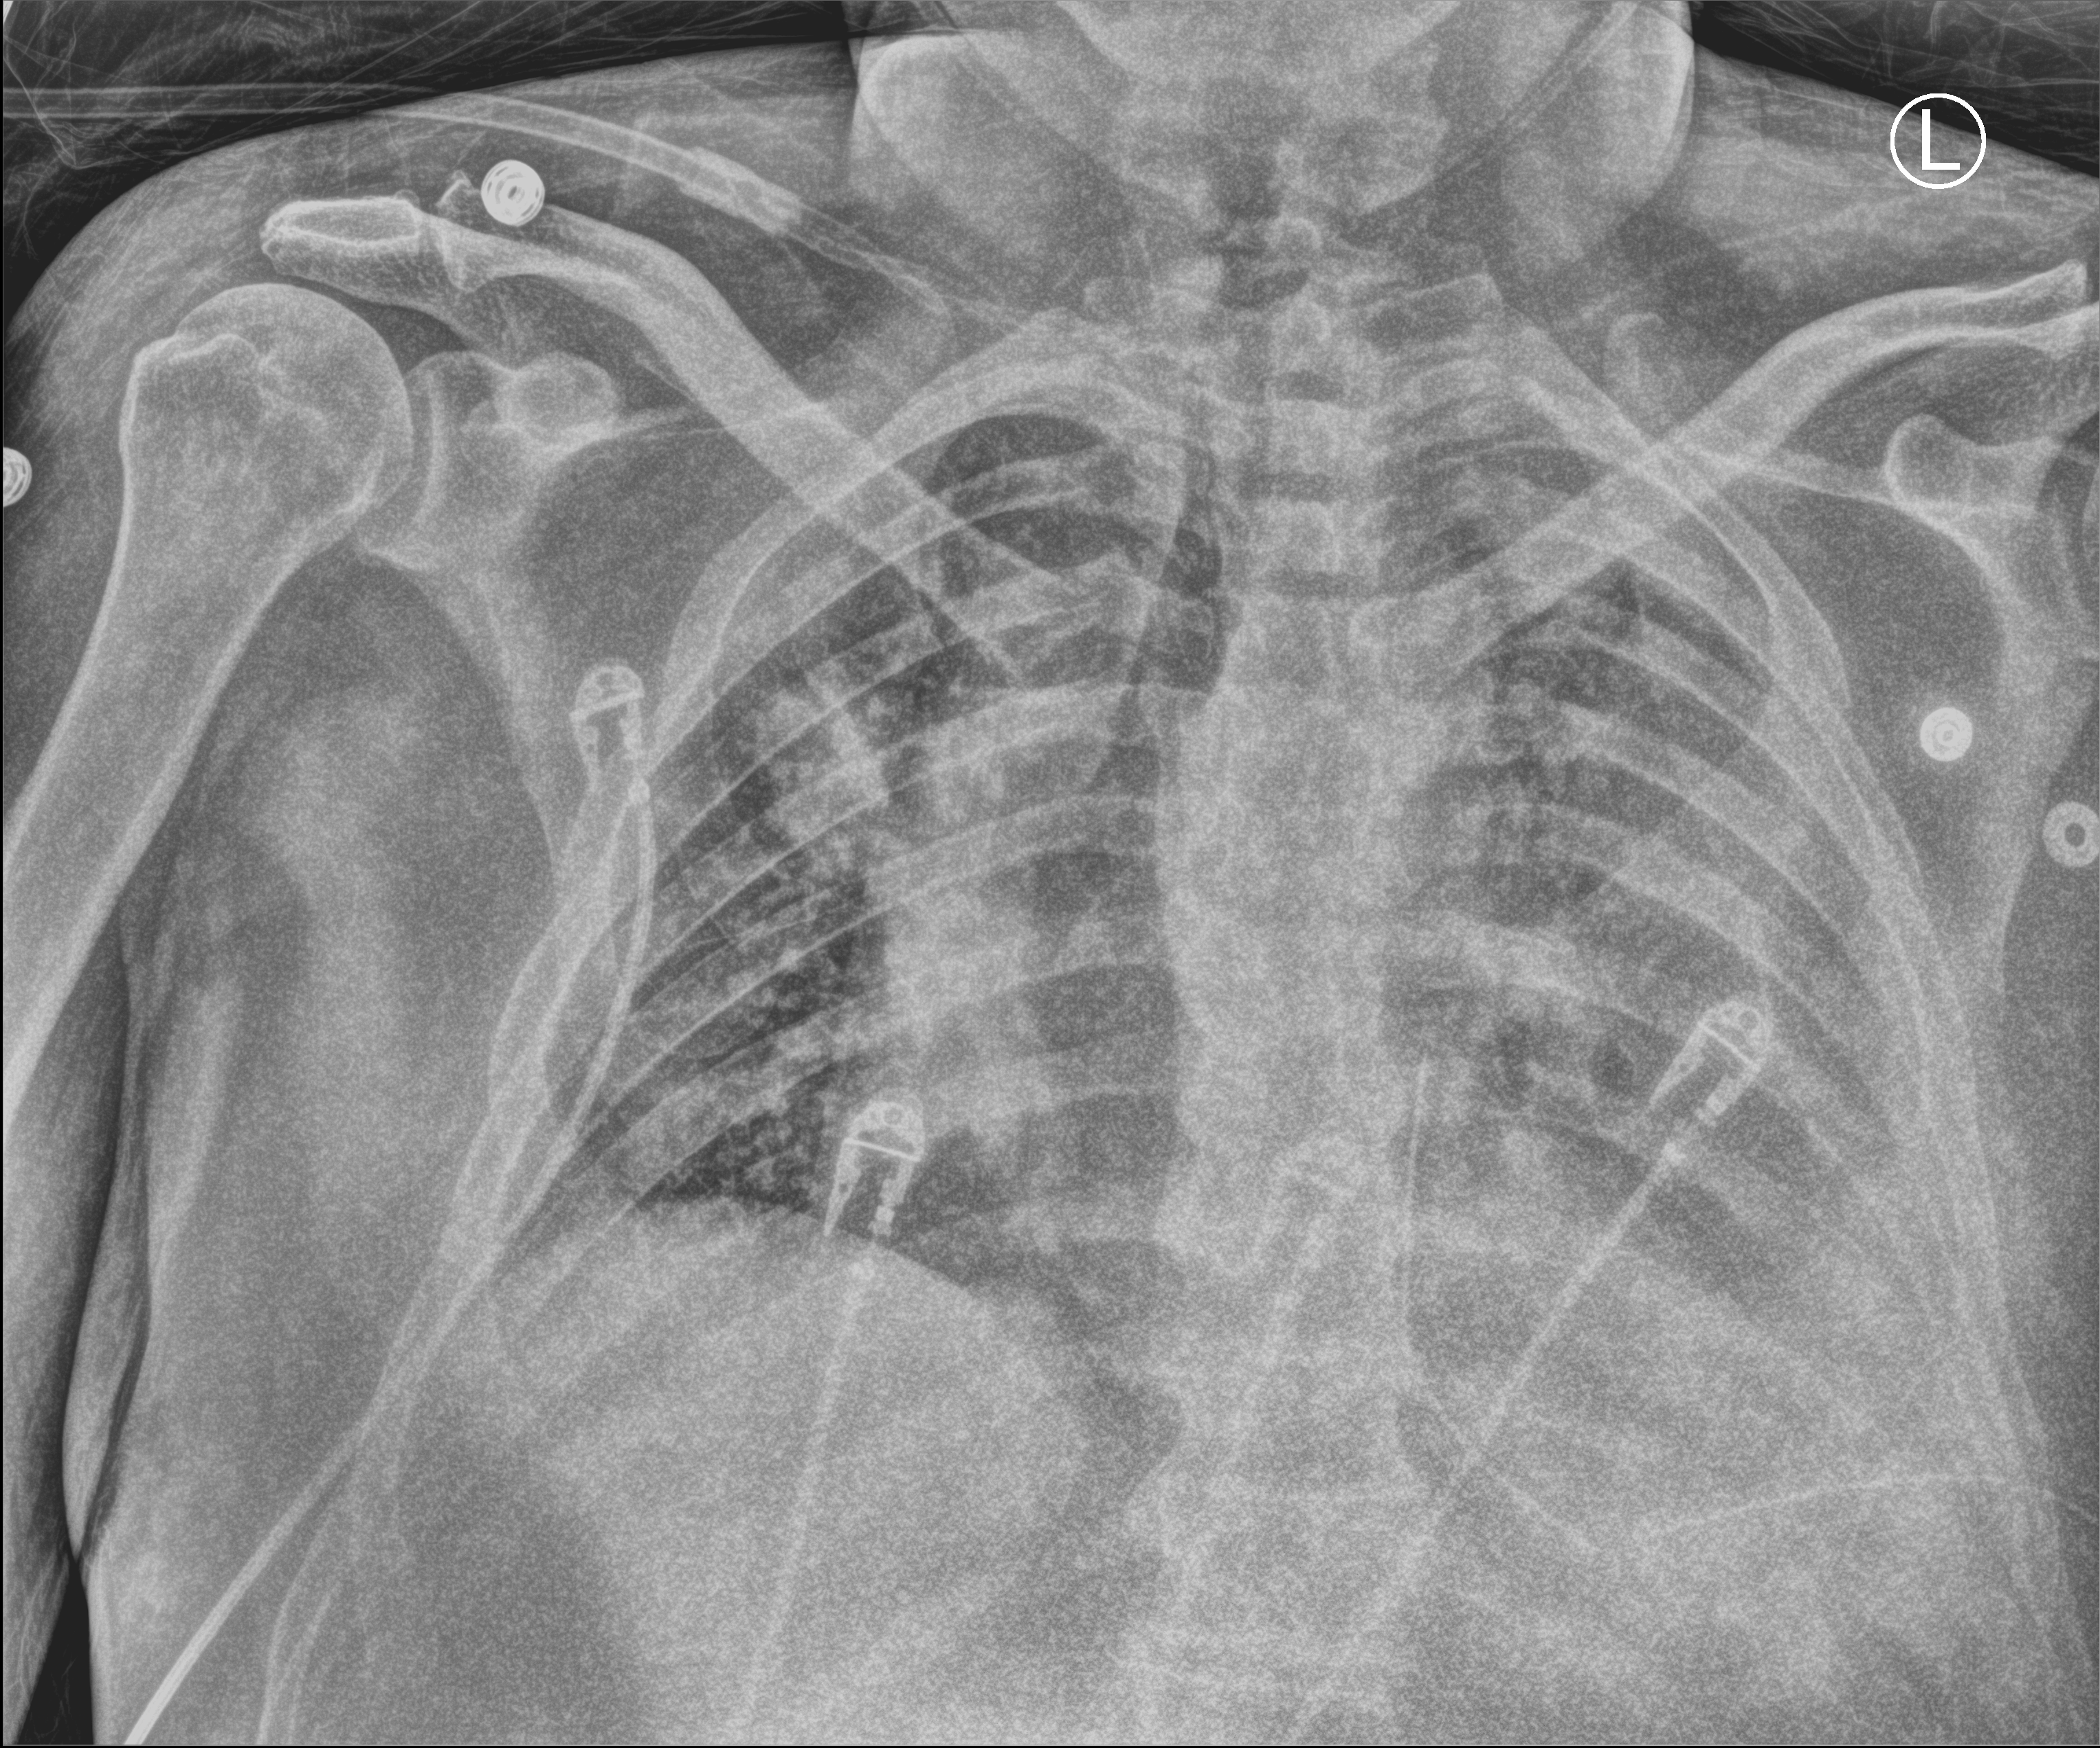
Portable chest radiograph; anteroposterior (AP) projection. Male patient hospitalised with COVID-19, age 18–59 years.
From the hospital-stay record, not from the radiograph (when in the stay this image was taken is not recorded): mechanically ventilated during this hospital stay: no.